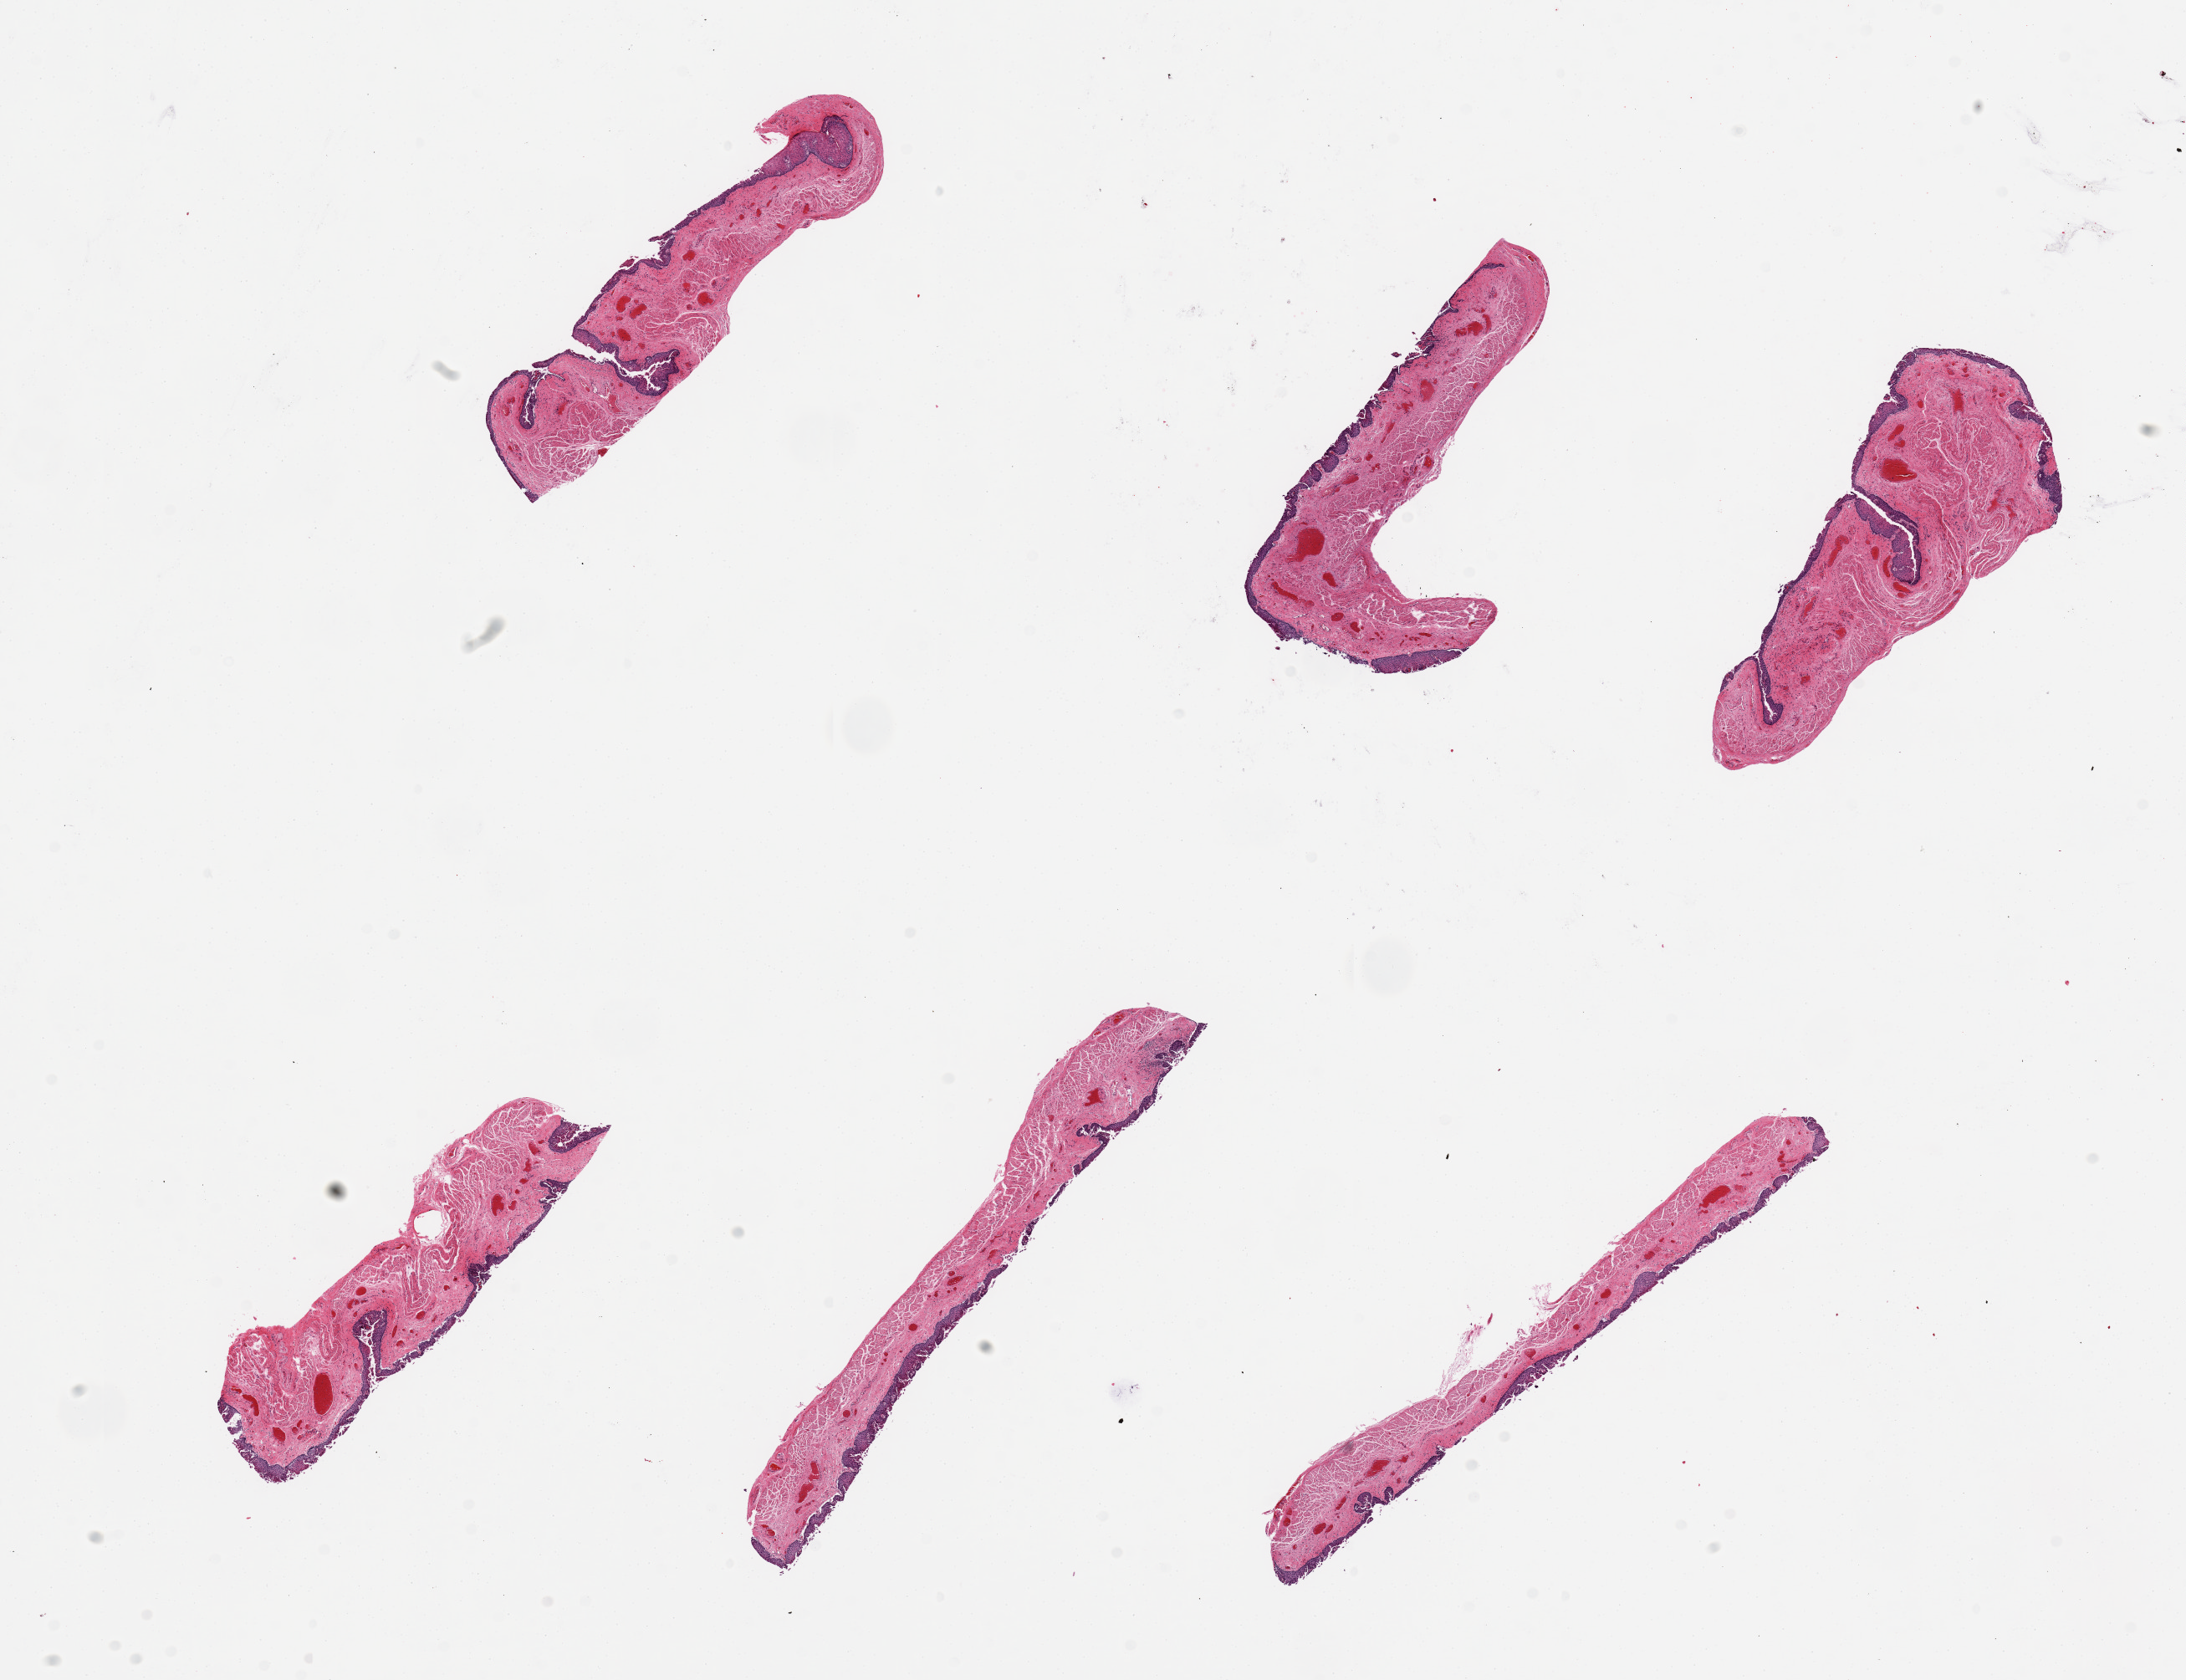
Whole-slide image, haematoxylin and eosin stain, brightfield, a low-resolution overview of the entire scanned area, about 20.7 x 15.9 mm (acquisition: 20x scan). PAXgene-fixed paraffin-embedded (PFPE) section. Sampled site (target tissue): esophageal mucous membrane. Tissue donor sample.
• reviewer comment on this tissue sample: 6 pieces; desquamation